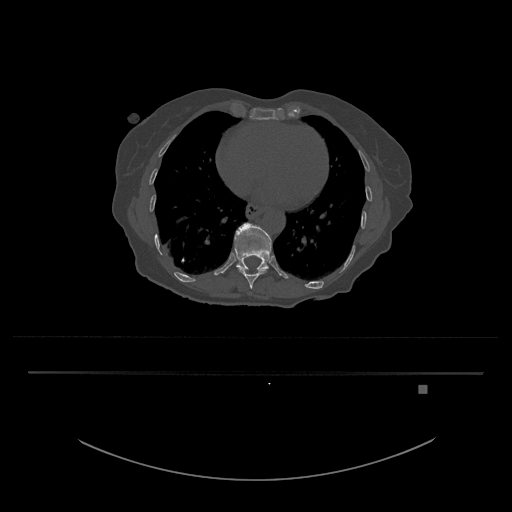
CT including the spine, one axial slice; slice 691 of 797 in the series (ordered by position); reconstruction kernel Br40s/3; 120 kVp; bone window (W 1800 / L 400 HU); 0.5 mm slice thickness; 512 × 512 image matrix, field of view 500 × 500 mm. Female patient, age 57 years. From the clinical record (not read from this slice): primary cancer: cervical.
Structures marked on this image (semi-automatic segmentation, software-assisted and operator-edited):
- T10 vertebra: bounding box [x1, y1, x2, y2] px = [238, 269, 267, 289]
- T11 vertebra: [234, 223, 272, 270]